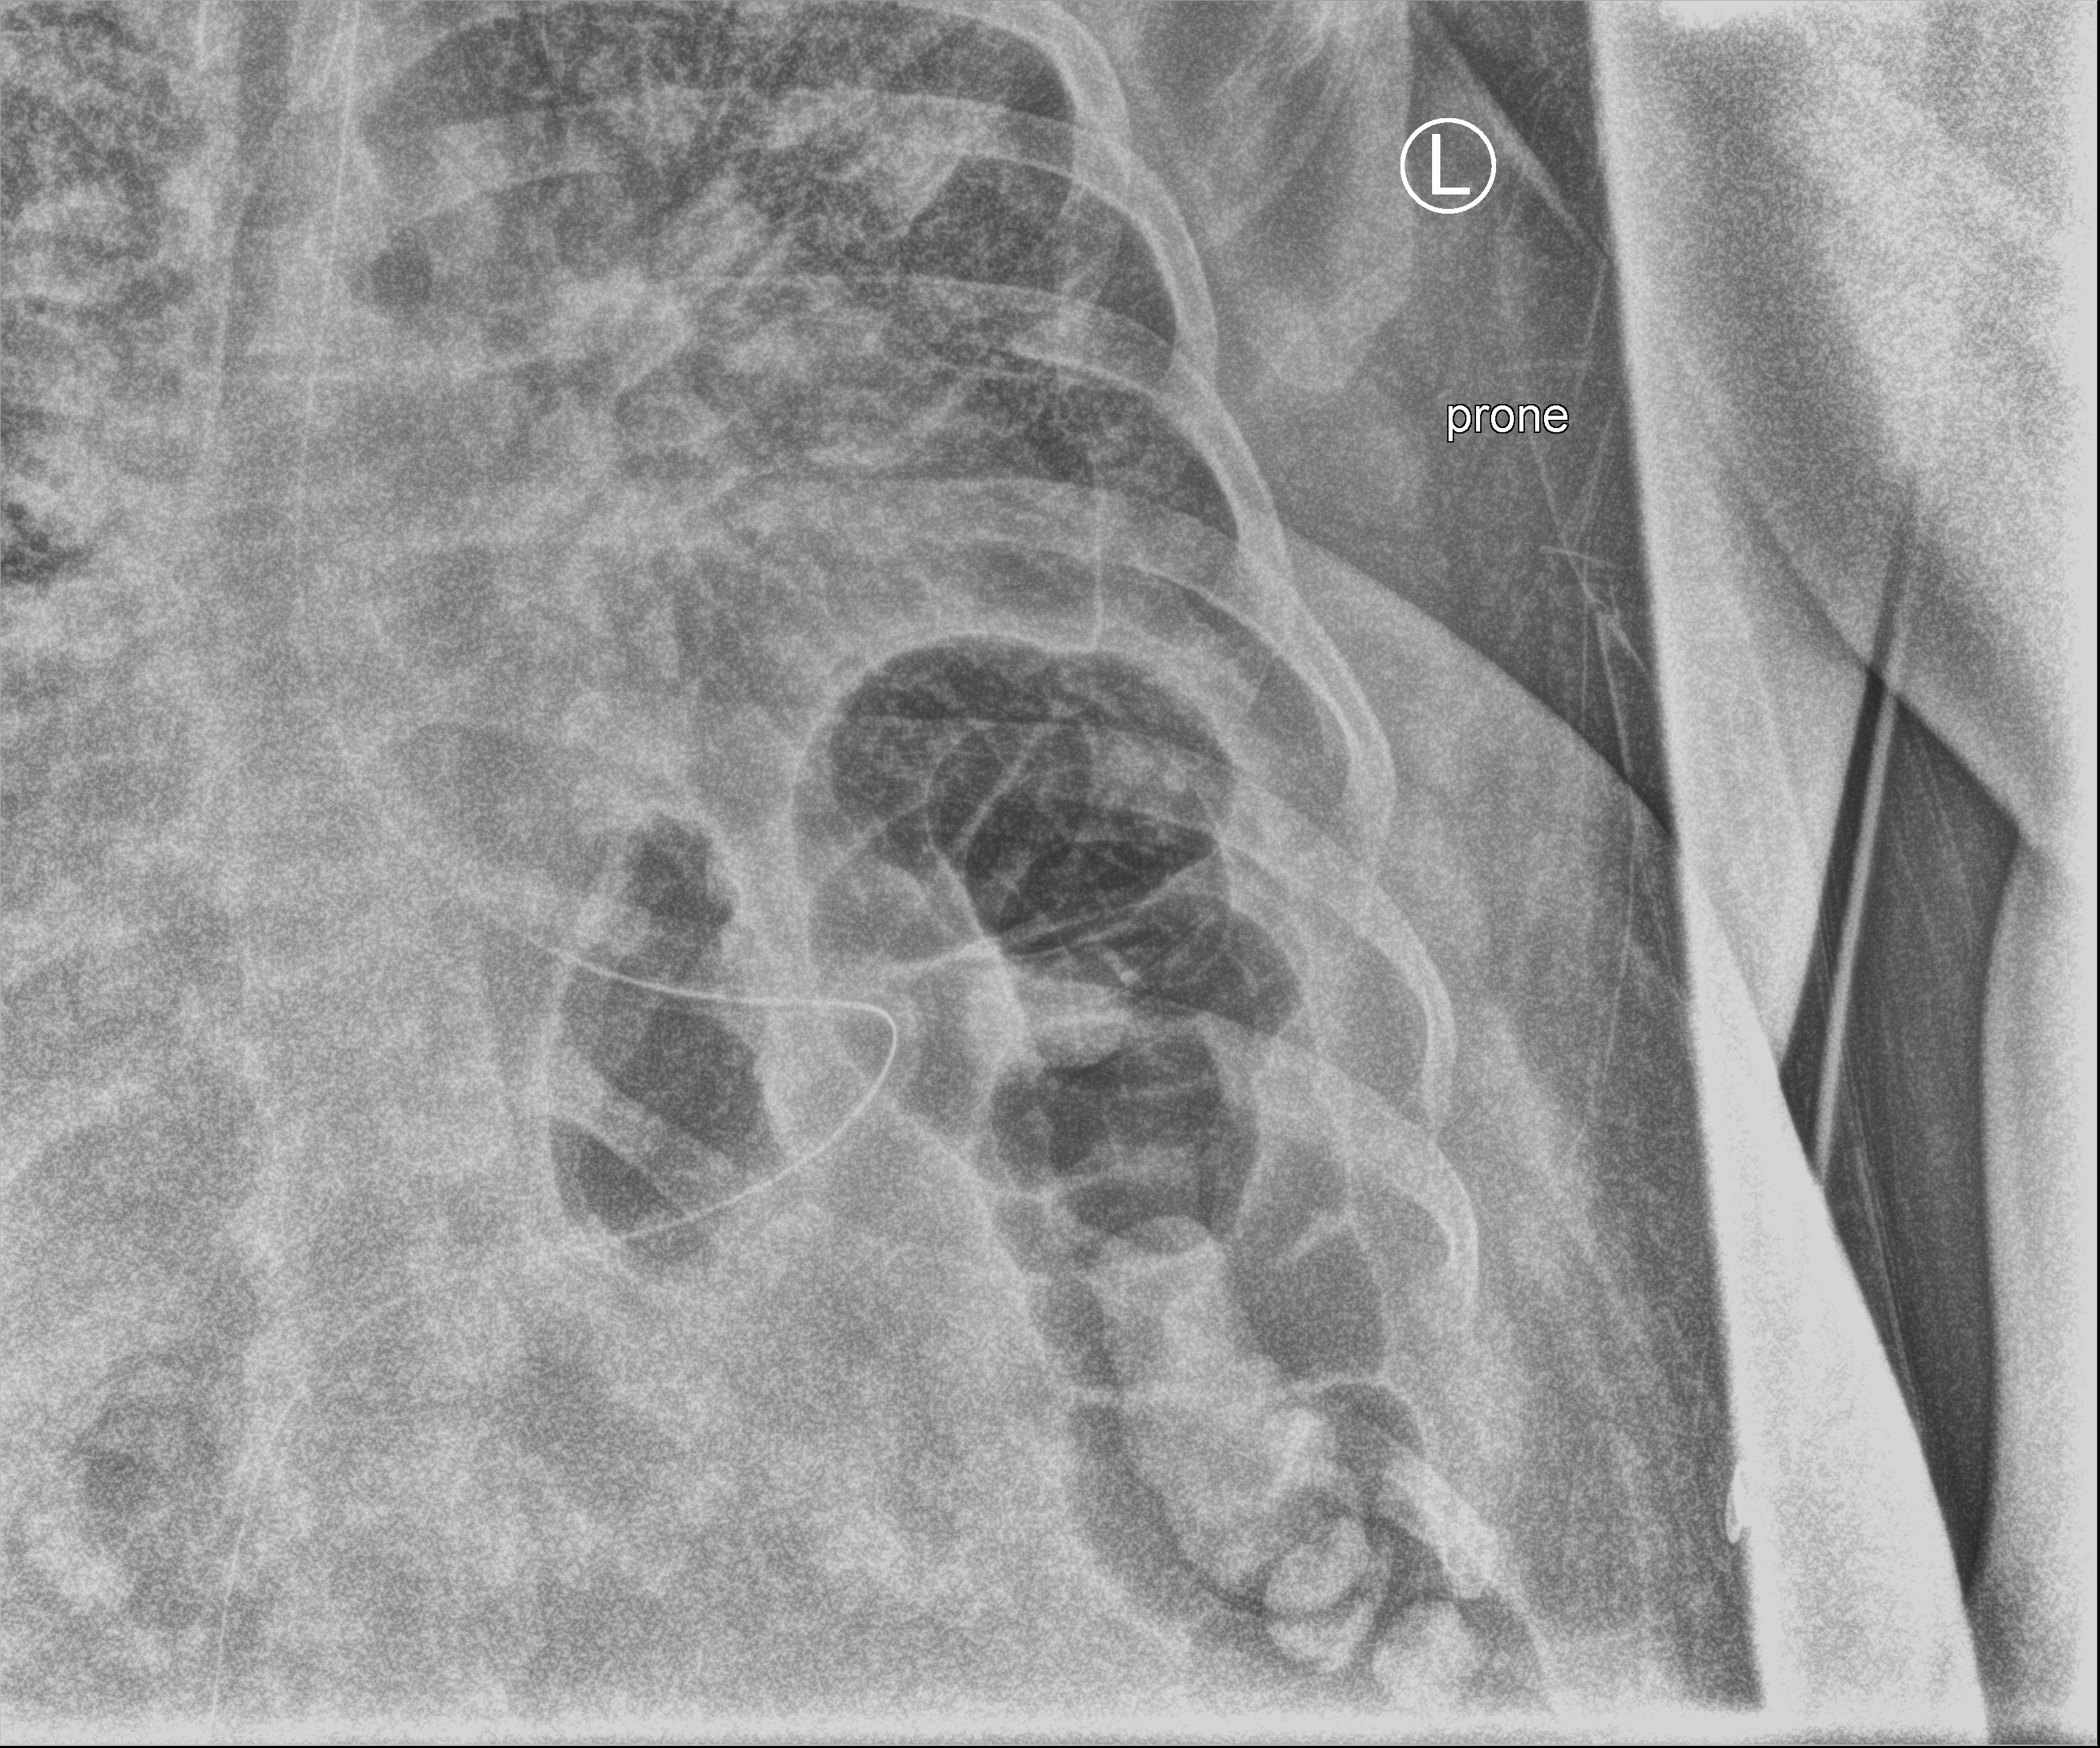
Chest X-ray (portable), anteroposterior (AP) projection. Patient hospitalised with COVID-19, aged 18–59 years.
From the hospital-stay record, not from the radiograph (when in the stay this image was taken is not recorded):
- admitted to intensive care during this hospital stay: yes
- length of hospital stay: 16 days
- mechanically ventilated during this hospital stay: yes